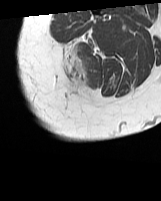
MRI of an extremity soft-tissue mass, one axial slice; position 10 of 70 along the scan axis; MR volume resampled by the dataset authors to the PET/CT grid (not the native acquisition matrix); 3.27 mm slice thickness; 161 × 201 image matrix, field of view 157 × 196 mm. Female patient. Case-level facts recorded for this patient, not image findings: histological type: synovial sarcoma; grade: intermediate; site of the primary tumour: right buttock.
Annotated regions visible in this slice (expert contour drawn on MRI and transferred to this co-registered scan by the dataset authors):
- gross tumour volume including surrounding oedema: bounding box <65,45,87,92> (left, top, right, bottom; pixels)